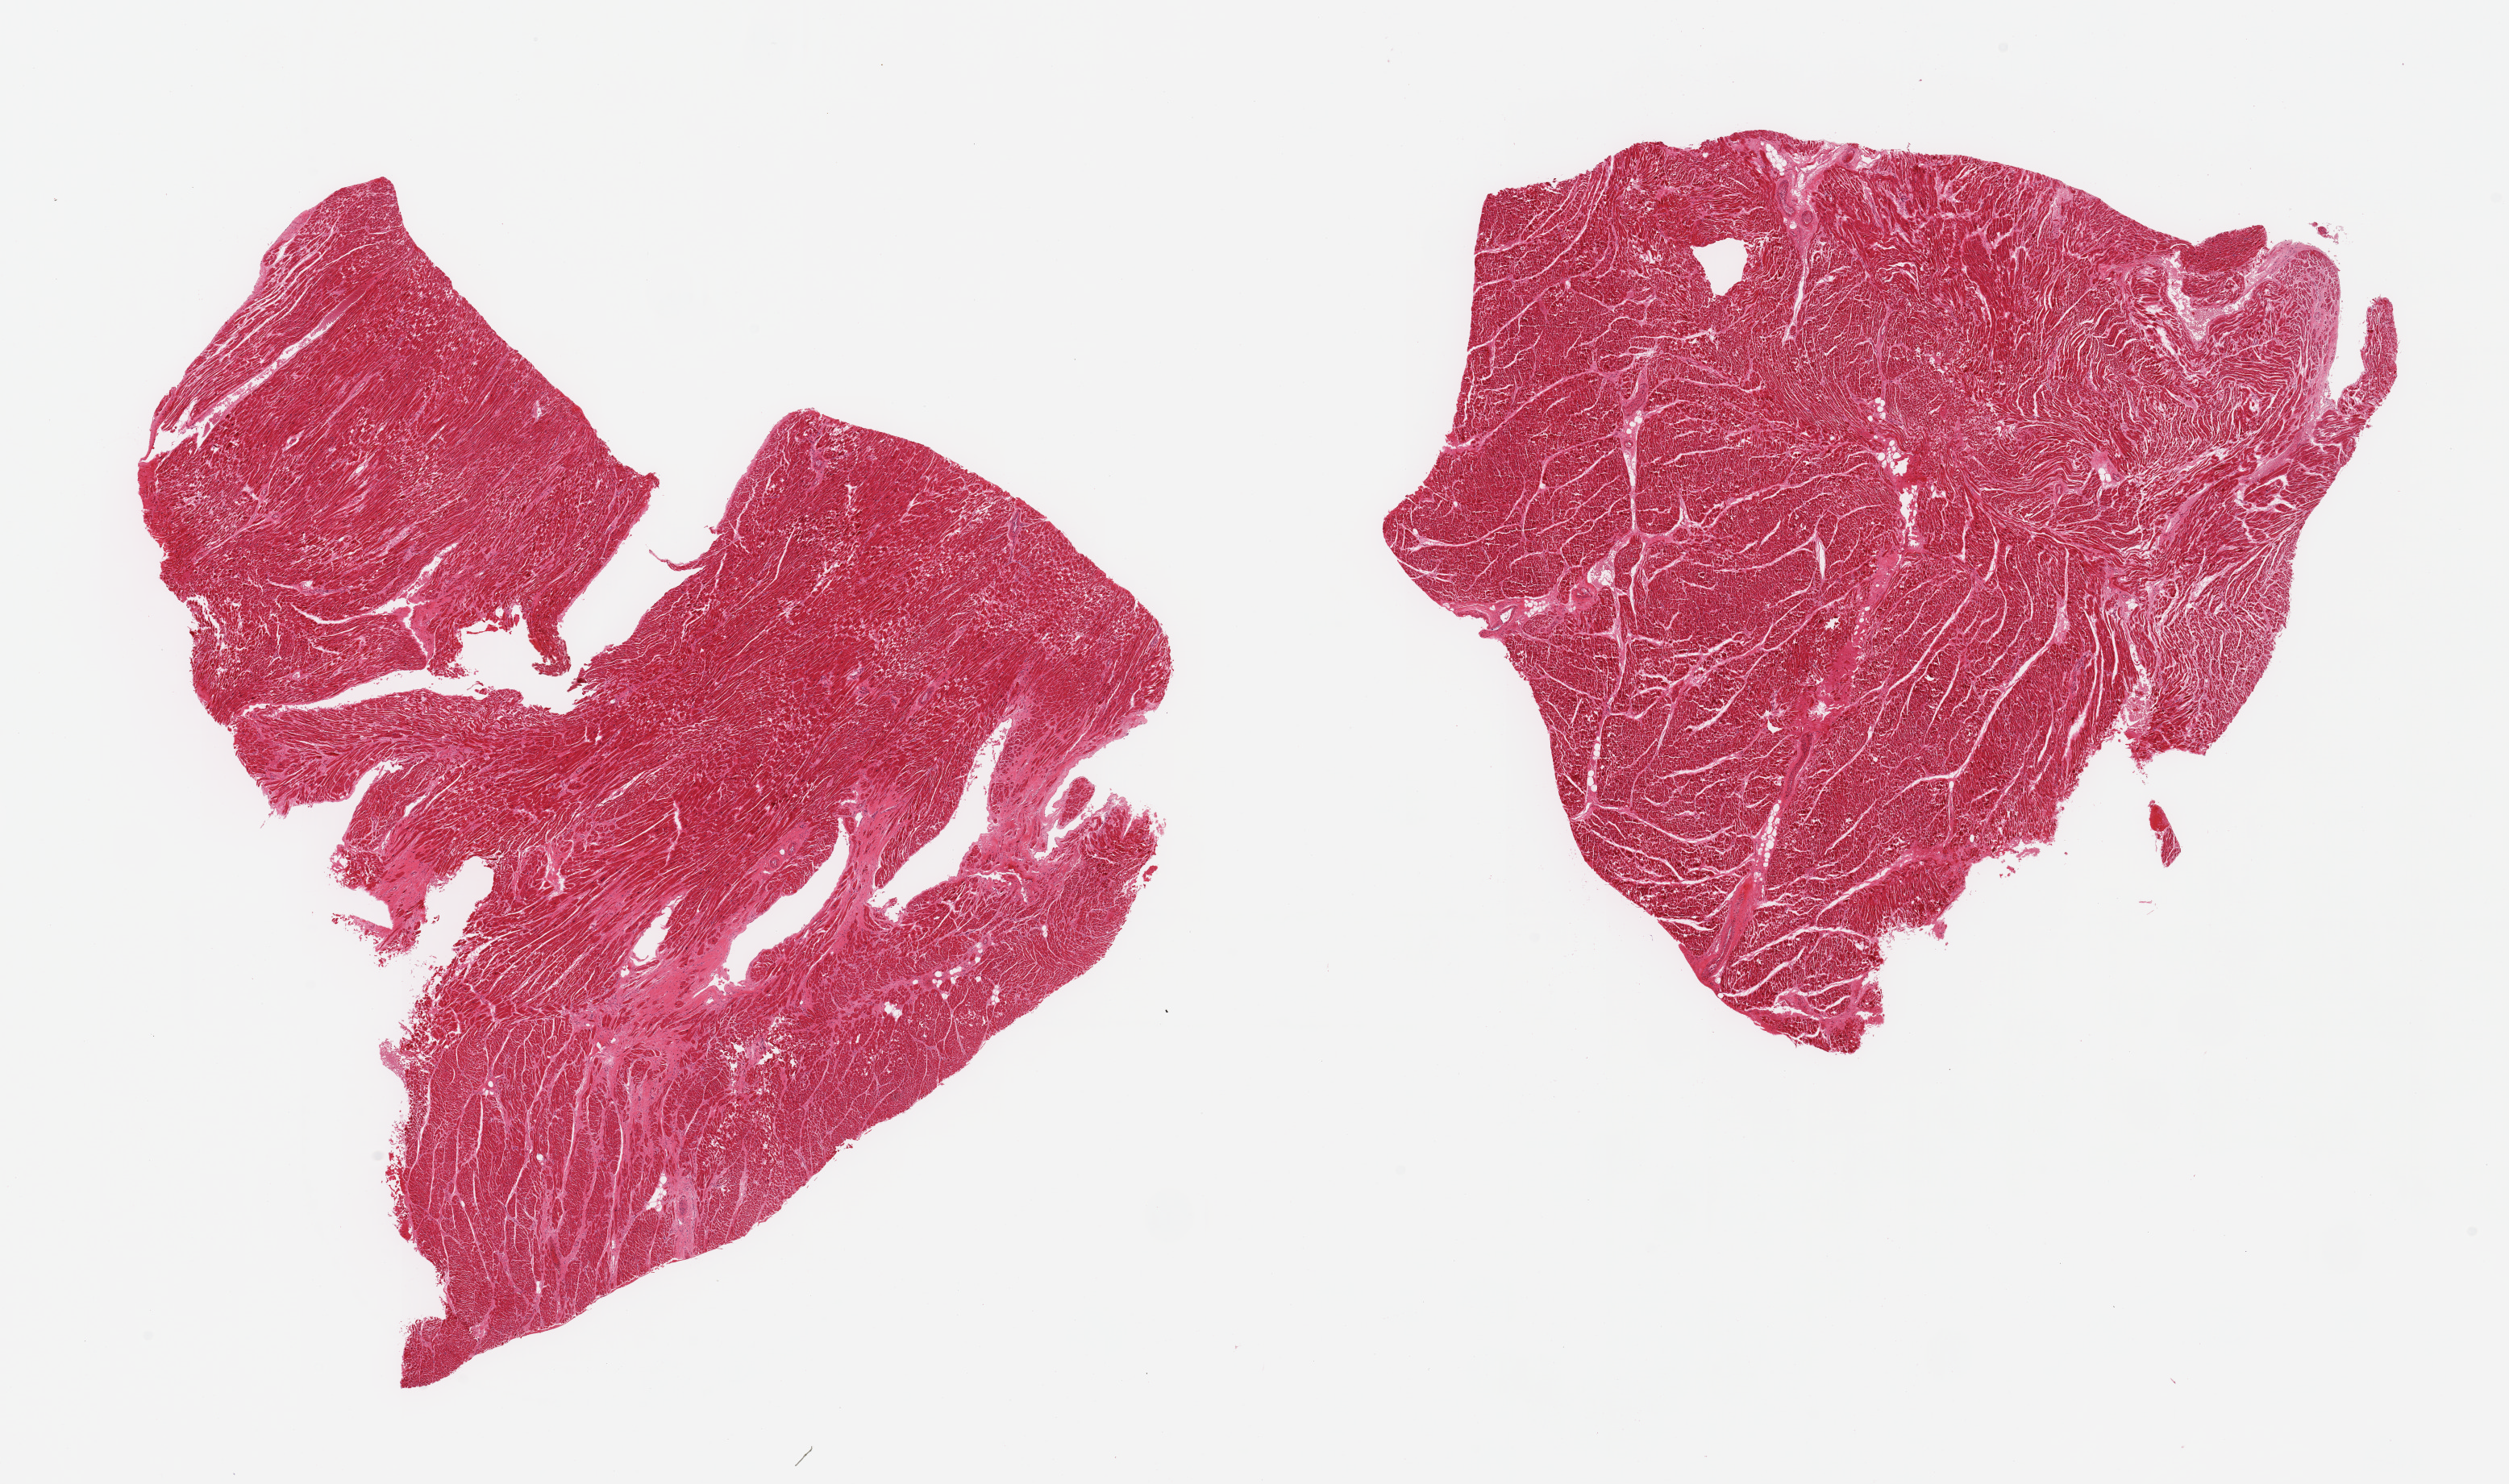
Whole-slide image, H&E stain — shown as a low-resolution overview of the whole scanned area (about 24.6 x 14.6 mm, slide scanned at 20x). PAXgene-fixed, paraffin-embedded tissue. Target tissue: heart. Donor tissue sample. Donor: male.
- pathologist's review note for this sample: 2 pieces; interstitial fibrosis with scarring, edema/fragmentation of fibers